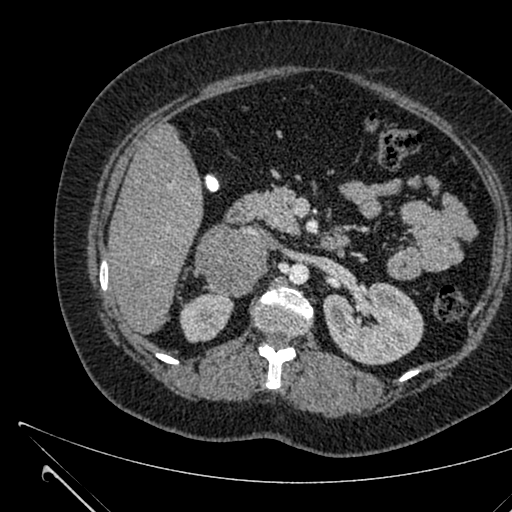
Contrast-enhanced abdominal CT, one axial slice; position 374 of 731 along the scan axis; 120 kVp; intravenous contrast given; soft-tissue window (W 400 / L 40 HU); 1 mm slice thickness; 512 × 512 image matrix, field of view 376 × 376 mm. Female patient, age 36 years. From the clinical record (not read from this slice): diagnosis: adrenocortical carcinoma; tumour side: right adrenal; tumour size at pathology: 10 cm; Ki-67 index: 20 %; stage (as recorded): 4.
Annotated regions visible in this slice (semi-automatically segmented with operator editing):
- mass: bounding box [x1, y1, x2, y2] px = [196, 225, 267, 296]